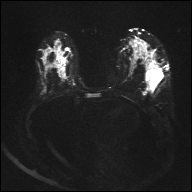
Breast MRI, one axial slice. Slice 19 of 32 in the series (ordered by position). Diffusion-weighted series; image 2 of 4 stored at this slice position (different b-values; order by instance number). 1.5 T. 192 × 192 image matrix, field of view 360 × 360 mm. Female patient.
Annotated regions visible in this slice (expert manual segmentation):
- tumour on diffusion-weighted imaging: bounding box <148,66,159,80> (left, top, right, bottom; pixels)